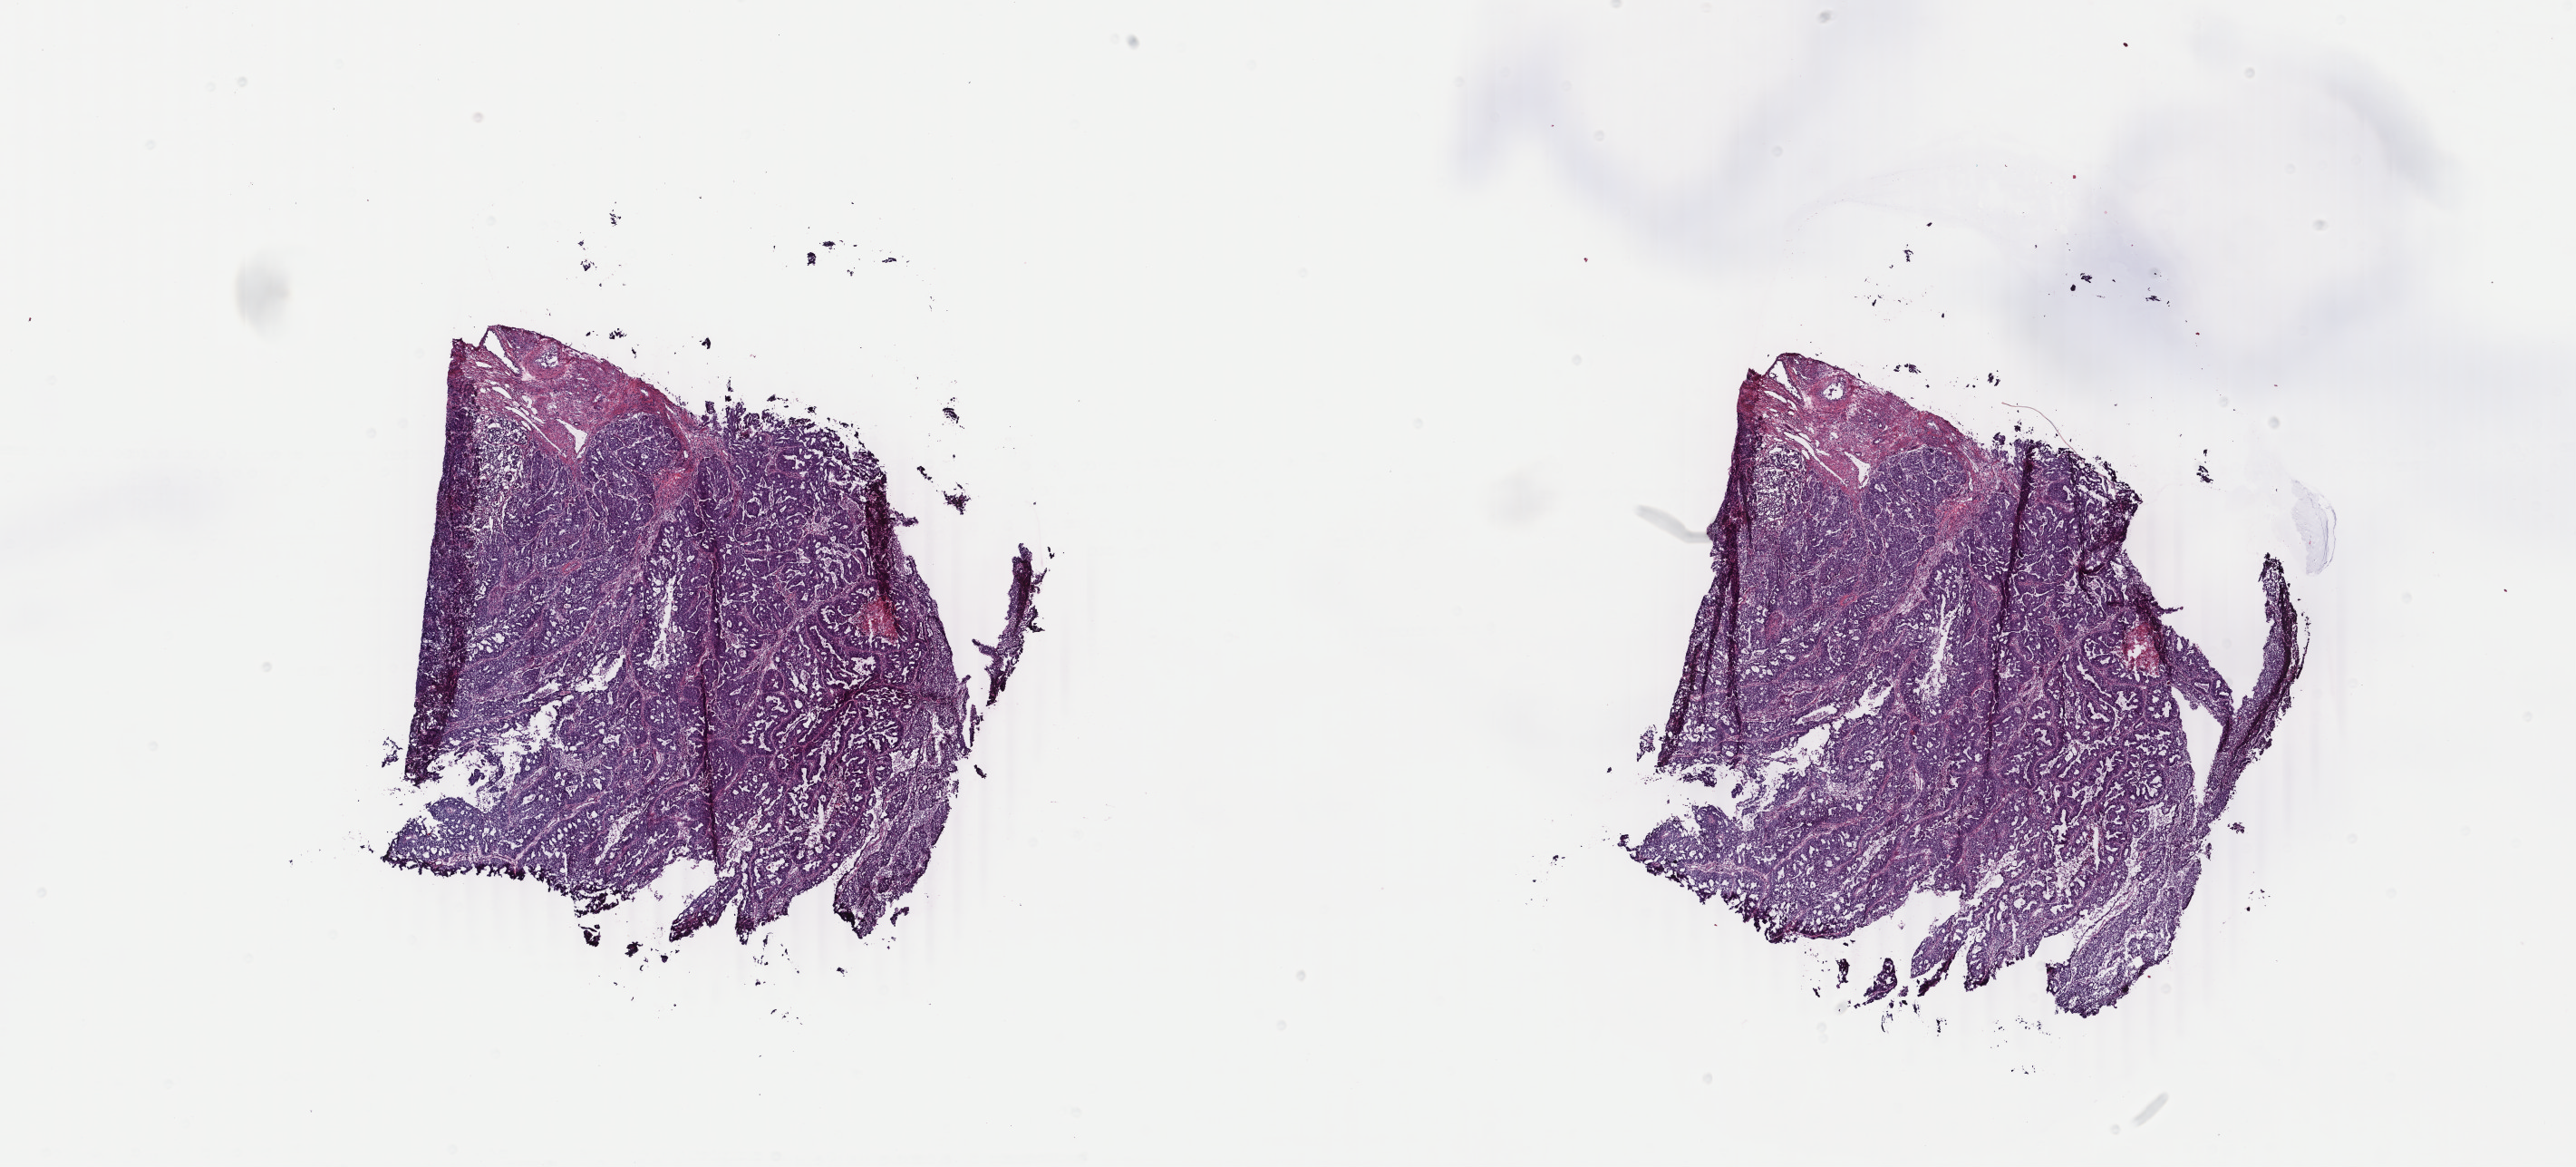
Whole-slide histology image, Hematoxylin and eosin (H&E) stained, shown as a low-resolution overview of the whole scanned area (about 22.6 x 10.2 mm, acquisition: 40x scan); frozen section; sample: primary tumour, uterus. Female, age 62 years at initial diagnosis. Histologic grade: G3 (poorly differentiated). Composition of this section per pathologist review: tumour cells 85%, tumour nuclei 85%, normal cells 0%, stromal cells 10%, necrosis 5%. Infiltration values recorded for this section: lymphocyte infiltration 0%, monocyte infiltration 0%, neutrophil infiltration 0%.
- pathologic diagnosis: Endometrioid adenocarcinoma, NOS (endometrium)
- lymph nodes positive (case pathology): 0 of 11 examined
- FIGO stage: IA